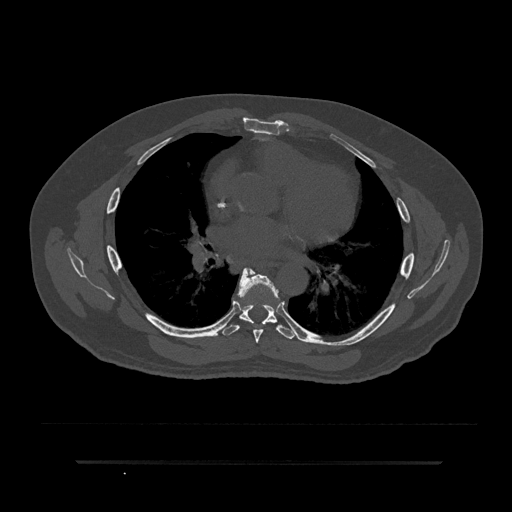
CT including the spine, one axial slice. Slice 503 of 797 in the series (ordered by position). Bone window (W 1800 / L 400 HU). 0.5 mm slice thickness. 512 × 512 image matrix. Male patient, age 59 years. Case-level facts recorded for this patient, not image findings: primary cancer: bile ducts.
Annotated regions visible in this slice (semi-automatic segmentation, software-assisted and operator-edited):
- T6 vertebra: bounding box <237,268,279,343> (left, top, right, bottom; pixels)
- T7 vertebra: <222,268,295,339>